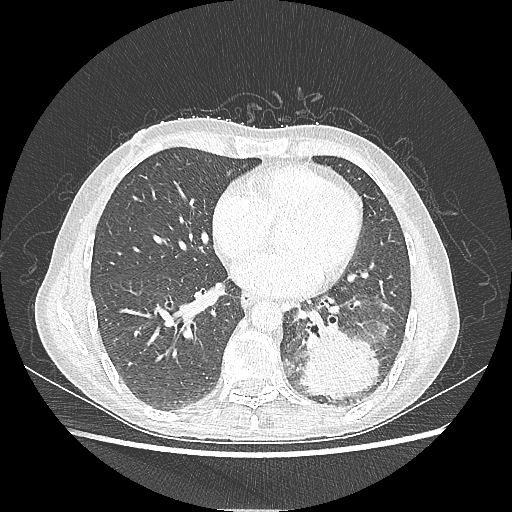
Chest CT, one axial slice; slice 92 of 220 in the series (ordered by position); lung window (W 1500 / L -600 HU); 1.25 mm slice thickness; 512 × 512 image matrix, field of view 360 × 360 mm. Female patient, age 53 years. Case-level facts recorded for this patient, not image findings: clinical TNM (as recorded): T3 N0 M0.
Structures marked on this image (bounding box drawn by a radiologist):
- lung tumour (recorded histology: adenocarcinoma): box from (x=298, y=328) to (x=381, y=403) px